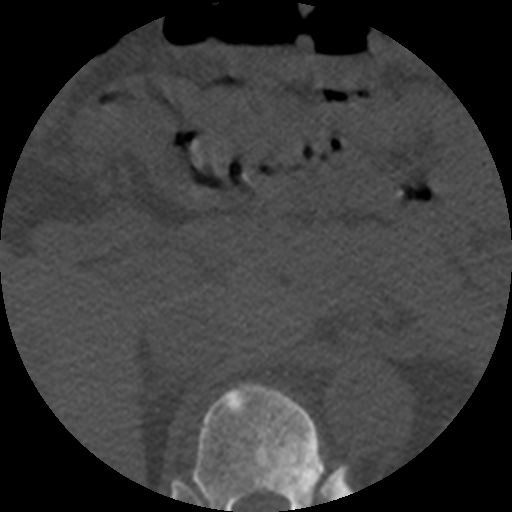
CT including the spine, one axial slice; slice 246 of 508 in the series (ordered by position); 120 kVp; bone window (W 1800 / L 400 HU); 512 × 512 image matrix. Patient age 57 years. Case-level facts recorded for this patient, not image findings: primary cancer: prostate.
Annotated regions visible in this slice (semi-automatic segmentation, software-assisted and operator-edited):
- T11 vertebra: bounding box <192,383,325,512> (left, top, right, bottom; pixels)